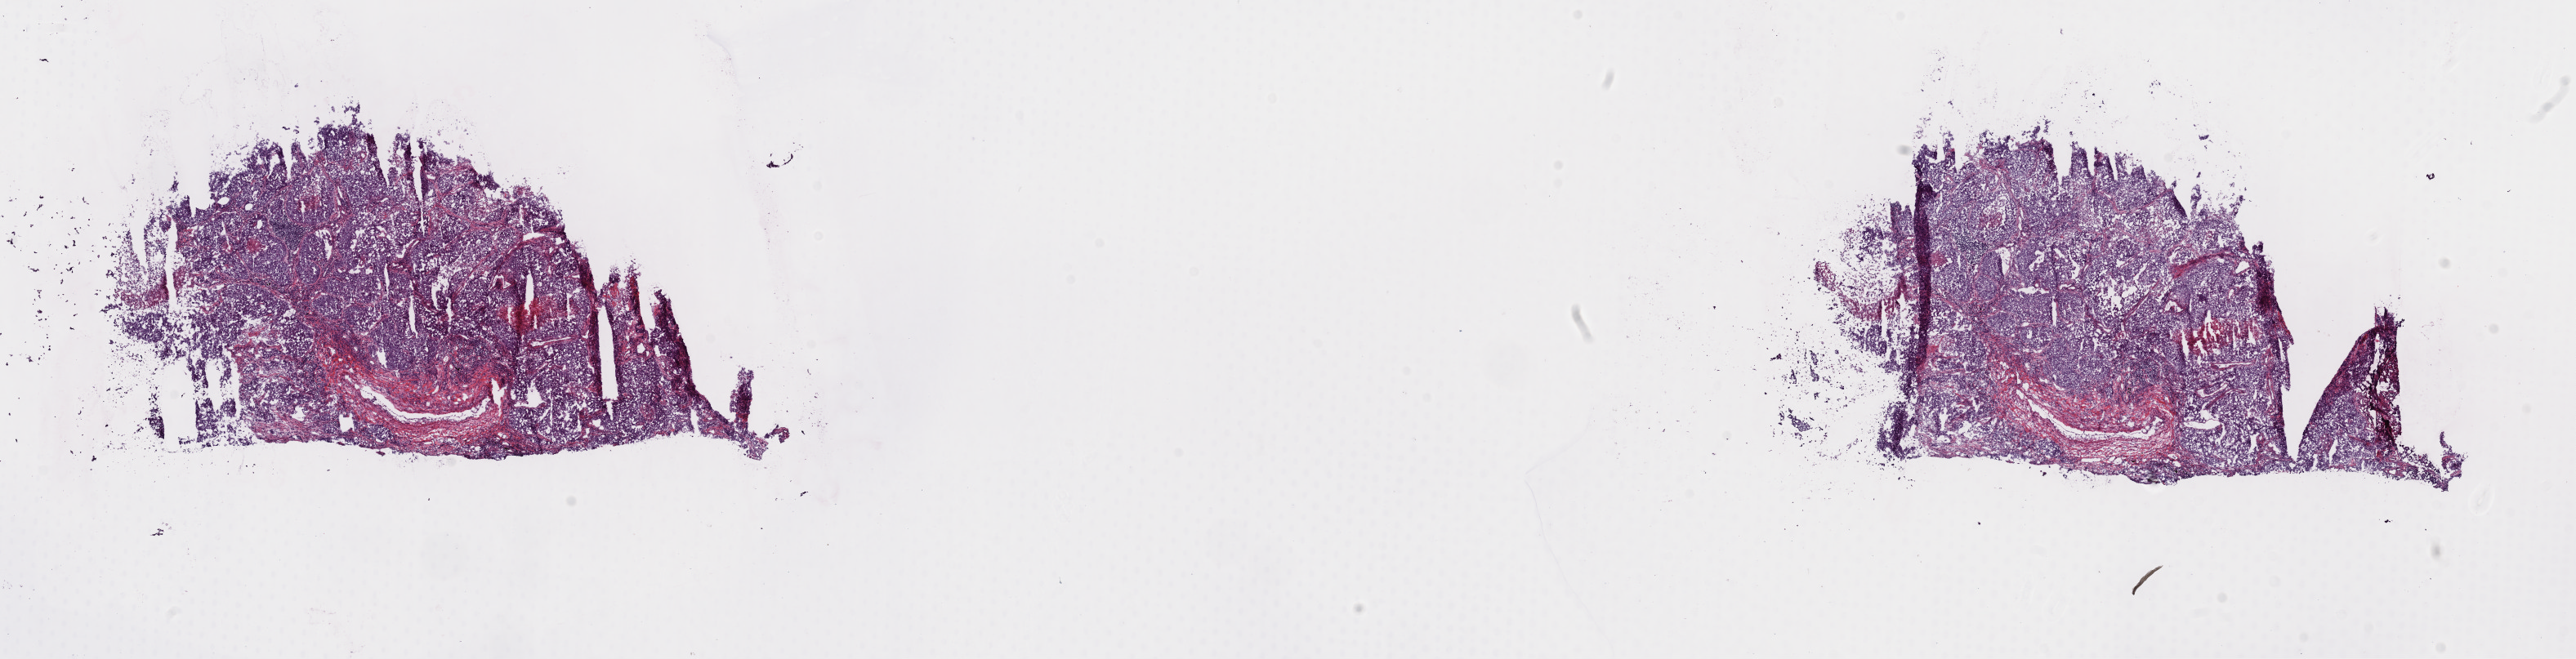
H&E-stained whole-slide image — a low-resolution overview of the entire scanned area, about 24.9 x 6.4 mm (acquisition: 40x scan); frozen section; lung, primary tumour sample. Male, age 63 years at initial diagnosis. Pathologist review of this section (percent, as recorded): tumour cells 65%, tumour nuclei 75%, normal cells 0%, stromal cells 25%, necrosis 10%. Inflammatory infiltration, as recorded: lymphocyte infiltration 5%, monocyte infiltration 0%, neutrophil infiltration 0%.
• laterality: left
• diagnosis: Acinar cell carcinoma (upper lobe, lung)
• AJCC pathologic stage: IIA (7th edition)